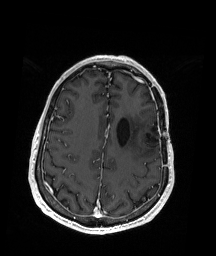
Brain MRI from a brain-tumour surgery series, one axial slice. Position 62 of 192 along the scan axis. T1-weighted post-contrast. 1 mm slice thickness. 216 × 256 image matrix, field of view 211 × 250 mm. From the clinical record (not read from this slice): histopathology: Oligodendroglioma; WHO grade: 2; IDH mutation: yes; tumour location: Left Insular.
Outlined on this slice (outlined manually by an expert reader):
- previous resection cavity: bounding box <132,124,163,146> (left, top, right, bottom; pixels)